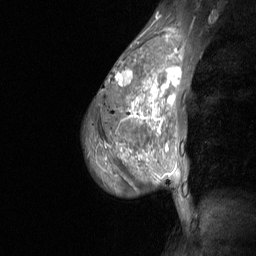
Breast MRI (dynamic contrast-enhanced), one sagittal slice; slice 45 of 64 in the series (ordered by position); dynamic contrast-enhanced study with each time point stored as its own series, time point 2 of 3 at this slice position (early post-contrast, ordered by acquisition time); 1.5 T; TE 4.8 ms, TR 27 ms; 256 × 256 image matrix, field of view 200 × 200 mm. Female patient, age 36 years. From the clinical record (not read from this slice): setting: breast cancer imaged before/during neoadjuvant chemotherapy; receptor status: HR-positive, HER2-negative.
Structures marked on this image (semi-automatic segmentation, software-assisted and operator-edited):
- analysis volume of interest (the breast-tissue region the enhancement analysis was run in; not a lesion): bounding box (x1, y1, x2, y2) in pixels: (84, 45, 187, 210)
- tumour enhancement mask (voxels above the 90 % enhancement threshold inside the analysis volume of interest): (116, 49, 182, 148)